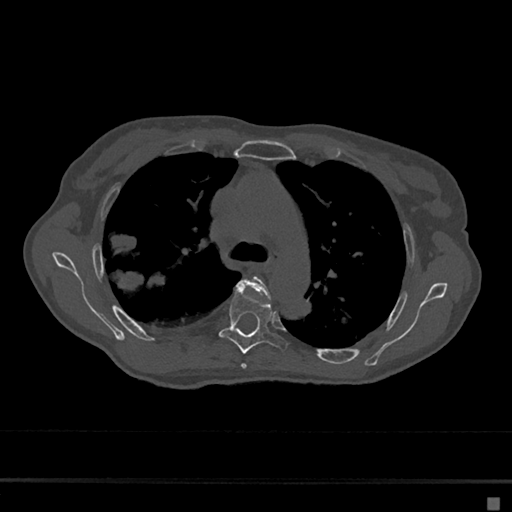
CT including the spine, one axial slice; position 467 of 797 along the scan axis; reconstruction kernel Br40s/3; 120 kVp; bone window (W 1800 / L 400 HU); 0.5 mm slice thickness; 512 × 512 image matrix, field of view 360 × 360 mm. Female patient, age 68 years. From the clinical record (not read from this slice): primary cancer: renal.
Annotated regions visible in this slice (semi-automatic segmentation, software-assisted and operator-edited):
- T4 vertebra: bounding box [x1, y1, x2, y2] px = [237, 276, 271, 369]
- T5 vertebra: [219, 289, 288, 354]